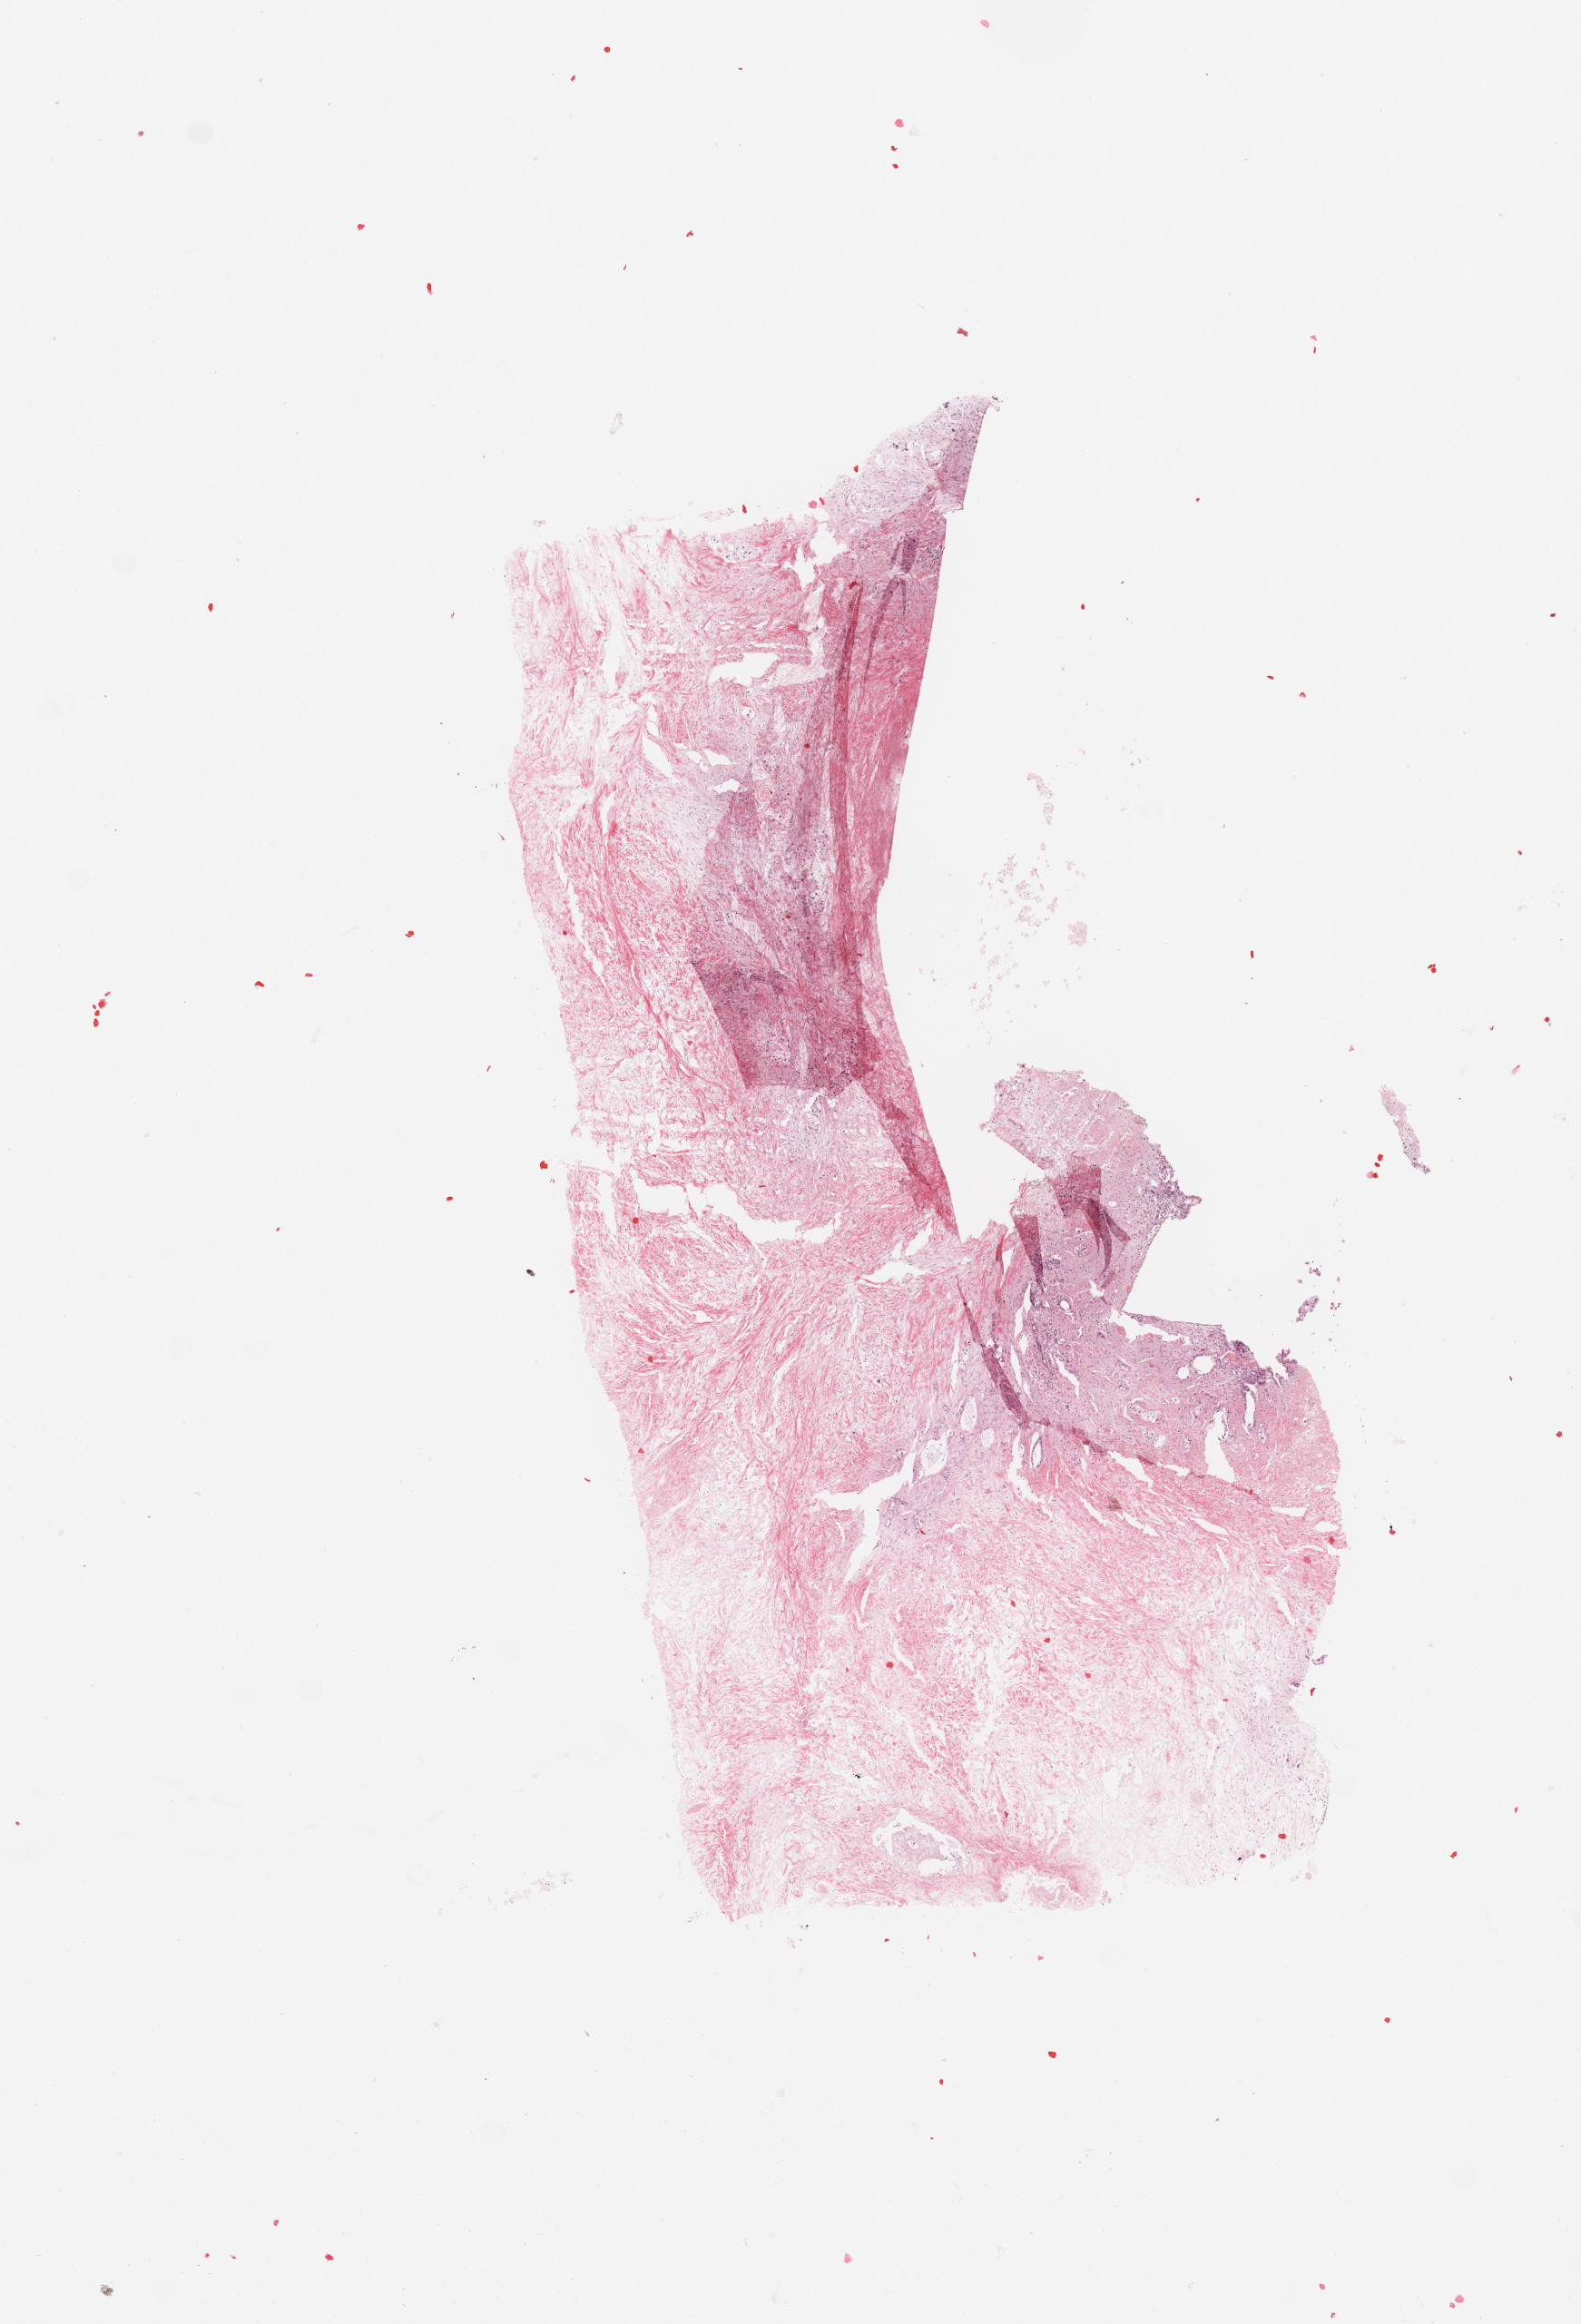
H&E whole-slide image, a low-resolution overview of the entire scanned area, about 6.9 x 10.1 mm (from a 20x scan), pancreas, tissue type not recorded.
Patient diagnosis (cohort enrolment): ductal adenocarcinoma (pancreas).